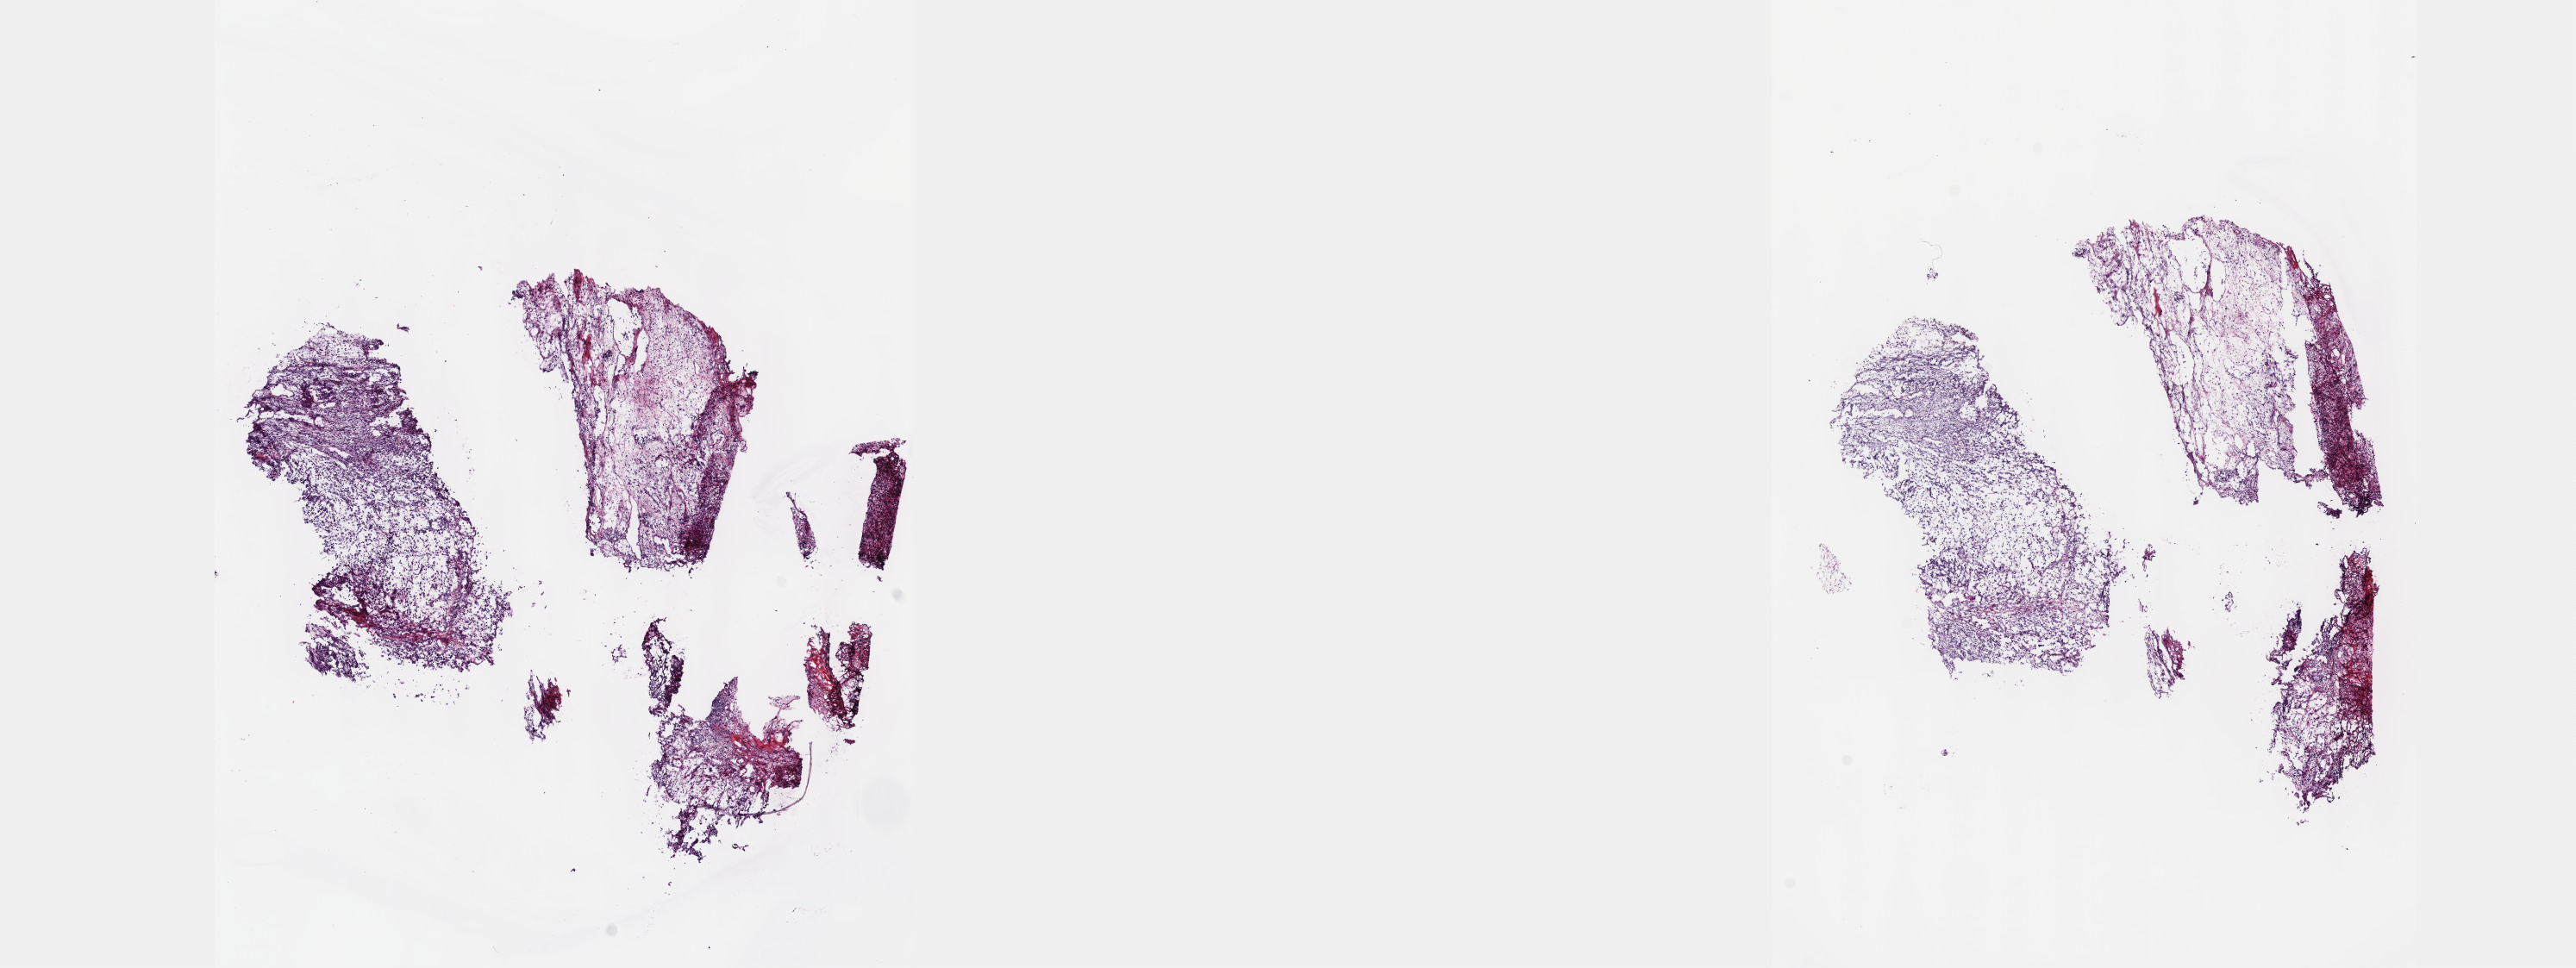
H&E-stained whole-slide image — low-resolution overview of the scanned area, about 24.1 x 9.1 mm; frozen section from the top of the tissue portion; sample: primary tumour, breast. Female patient; age at initial diagnosis 56 years. Pathologist review of this section (percent, as recorded): tumour cells 60%, tumour nuclei 60%, normal cells 20%, stromal cells 10%, necrosis 10%. Inflammatory infiltration, as recorded: lymphocyte infiltration 5%, monocyte infiltration 2%, neutrophil infiltration 2%.
- AJCC pathologic stage: IIB
- lymph nodes positive (case pathology): 0 of 1 examined
- laterality: left
- diagnosis: Metaplastic carcinoma, NOS
- TNM: T3 N0 MX